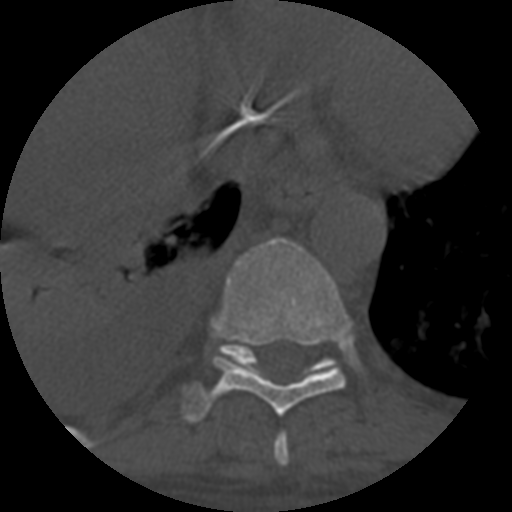
CT including the spine, one axial slice; slice 374 of 708 in the series (ordered by position); reconstruction kernel STANDARD; one of 3 acquisitions stored at this slice position; bone window (W 1800 / L 400 HU); 1.25 mm slice thickness; 512 × 512 image matrix, field of view 160 × 160 mm. Patient age 55 years. Case-level facts recorded for this patient, not image findings: primary cancer: colon; vertebrae with lytic lesions (as recorded): T12, L1, L5.
Structures marked on this image (semi-automatically segmented with operator editing):
- T10 vertebra: box from (x=221, y=344) to (x=335, y=376) px
- T8 vertebra: (x=274, y=433)–(x=289, y=466)
- T9 vertebra: (x=184, y=238)–(x=351, y=423)